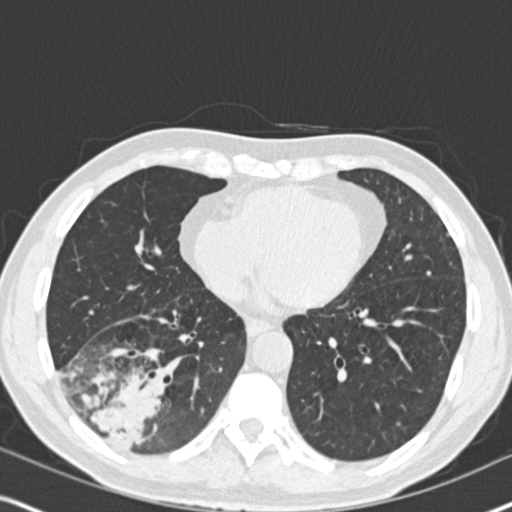
Axial slice from a low-dose chest CT screening exam, second annual screen, lung window (W 1500 / L -600 HU), 2 mm slice thickness, standard (soft-tissue) reconstruction kernel (B30f), slice 107 of 182 in the series, 512 × 512 image matrix, field of view 330 × 330 mm. Male, age 61 years at enrolment. Current smoker at enrolment.
• Lesion marked by an expert reader, bounding box (x1, y1, x2, y2) in pixels: (51, 328, 189, 464).
• Screening reader's record for this exam (one nodule recorded; not confirmed to be the boxed lesion): non-calcified nodule or mass ≥4 mm, right lower lobe, 90 × 80 mm, soft tissue attenuation, pre-existing on the prior screen: yes; interval growth: yes.